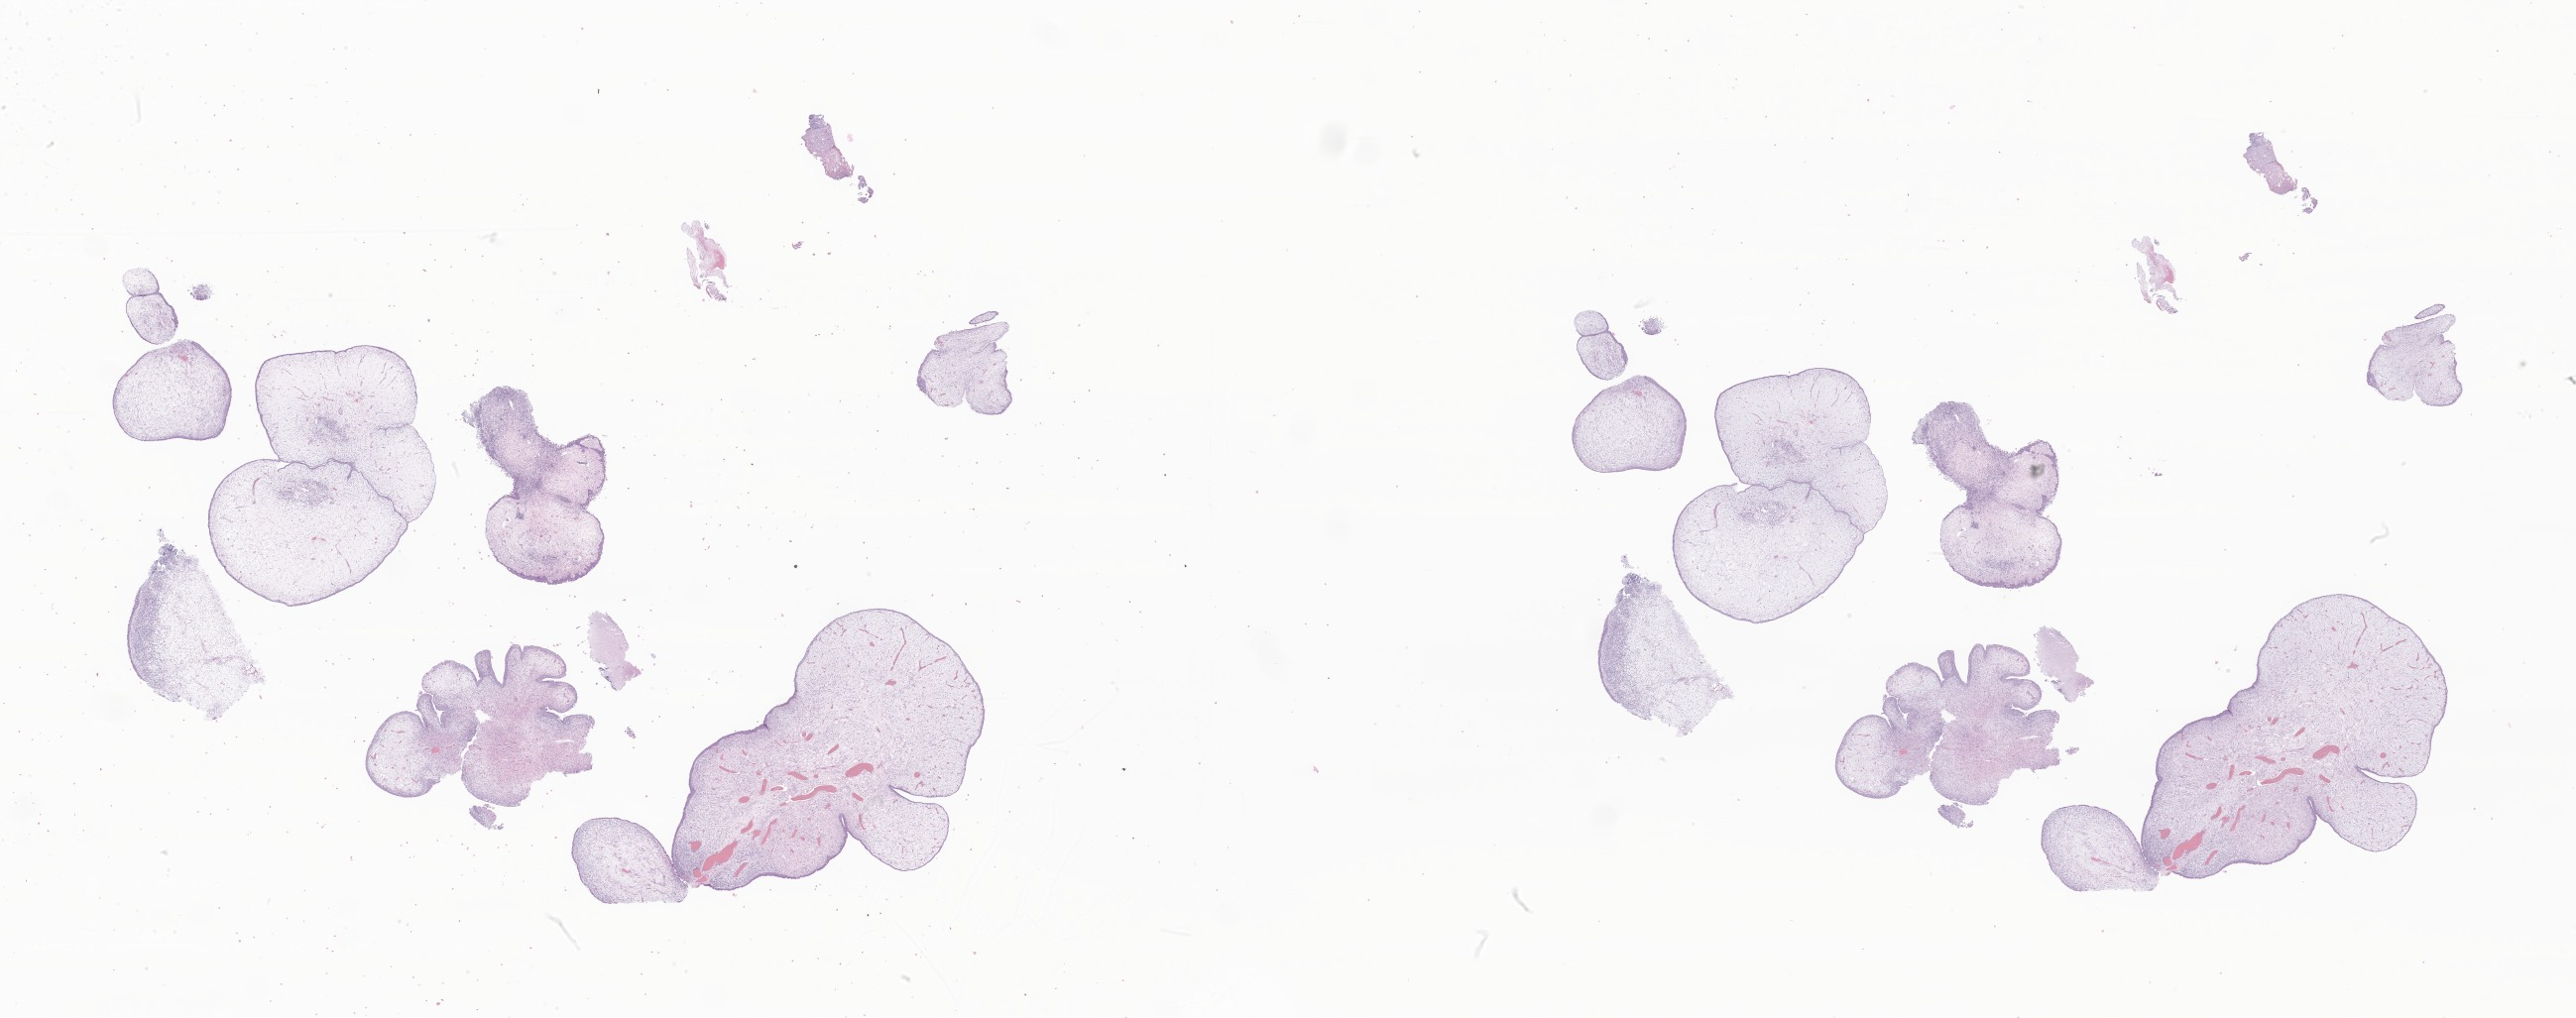
Whole-slide image, H&E stain of tumor tissue from the urinary bladder — low-resolution overview of the scanned area, about 43.8 x 17.3 mm; formalin-fixed, paraffin-embedded (FFPE) tissue. Patient female; age 55 months (4 years 7 months).
Diagnosis: Embryonal rhabdomyosarcoma, NOS.